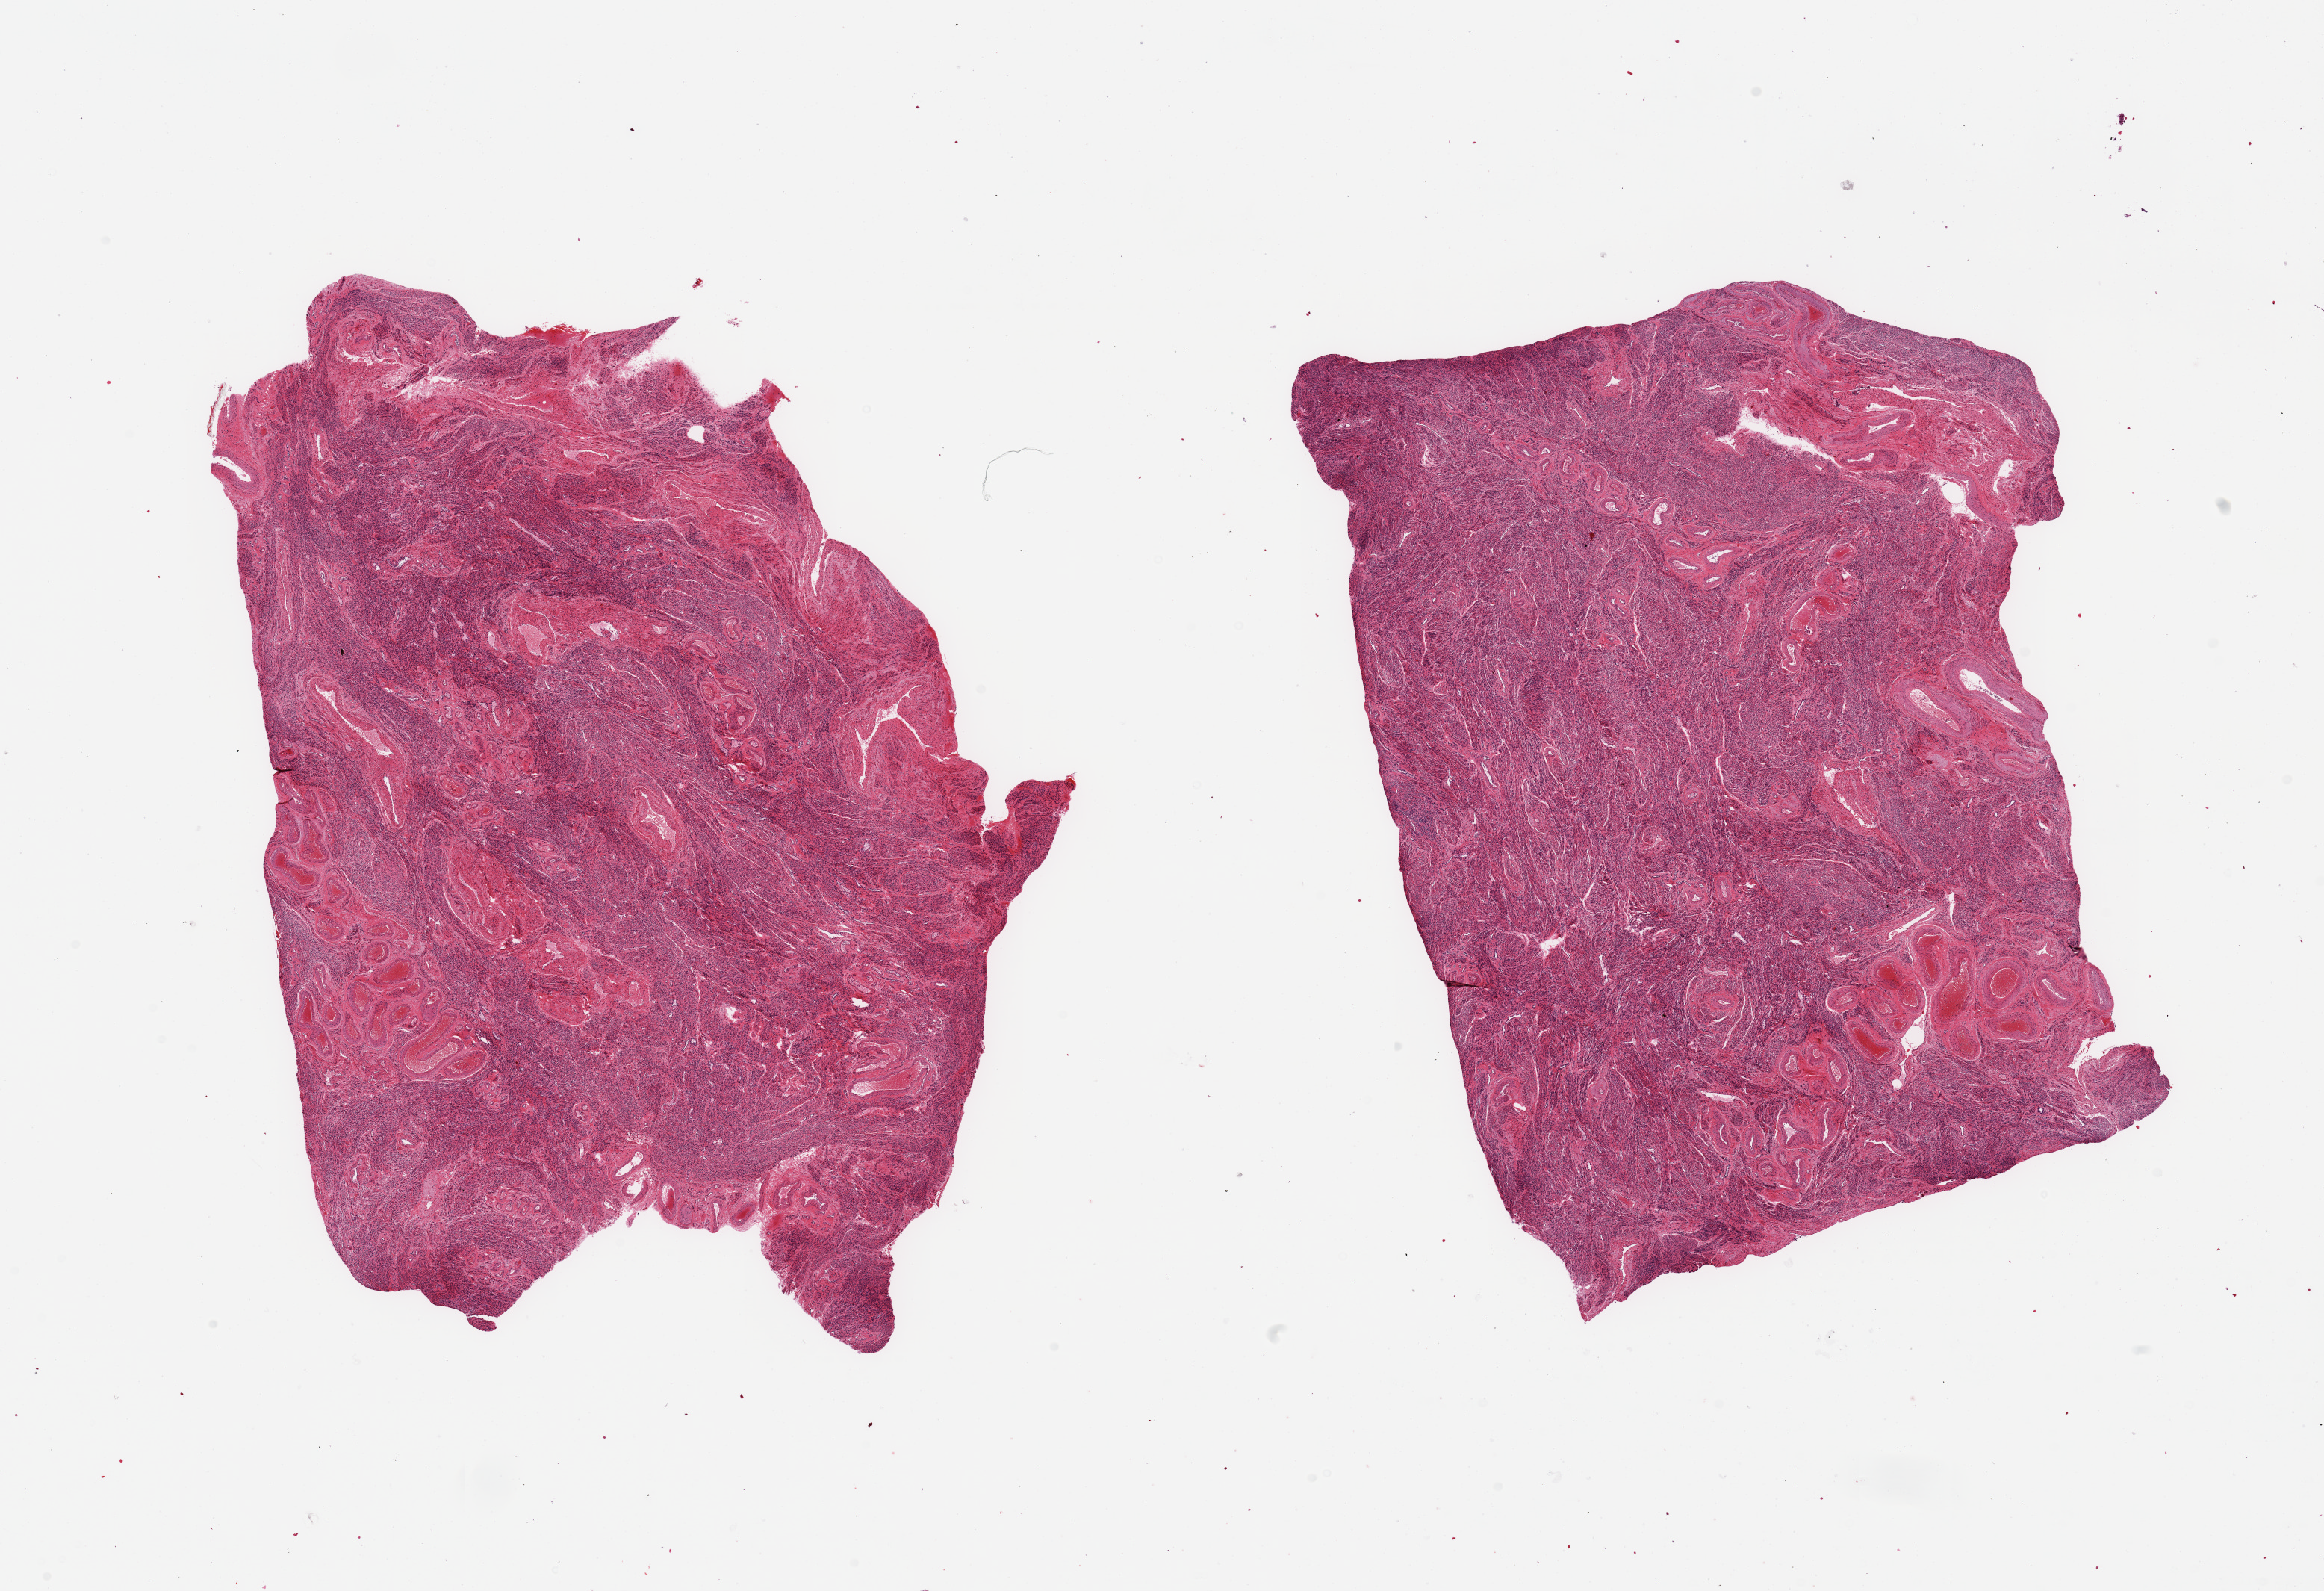
Hematoxylin and eosin (H&E) whole-slide image — low-resolution overview of the scanned area, about 24.6 x 16.8 mm (acquisition: 20x scan), PAXgene-fixed paraffin-embedded (PFPE) section, sampled site (target tissue): uterus, donor tissue sample. Donor: female.
- review note (as recorded): 2 pieces; all myometrium (in this cut) no endometrium